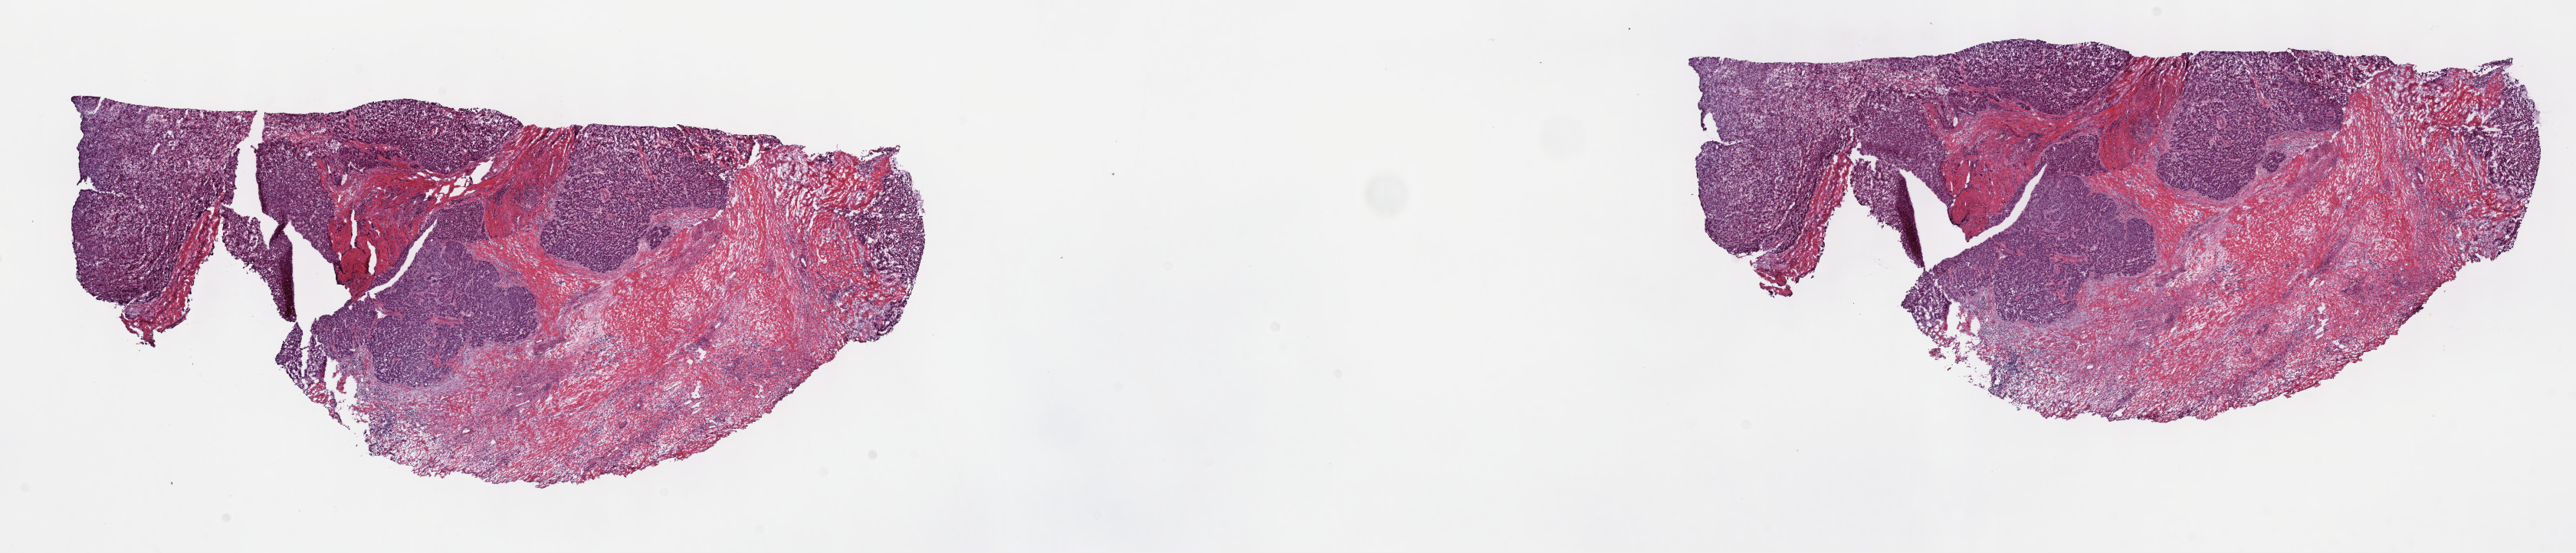
Digitized H&E-stained tissue section (whole slide) — whole scanned area (about 27.2 x 5.8 mm, from a 40x scan) shown as a low-resolution overview; frozen section from the top of the tissue portion; sample: primary tumour, liver. Female patient; age at initial diagnosis 65 years. Histologic grade: G2 (moderately differentiated). Slide review estimates, as recorded: tumour cells 50%, tumour nuclei 60%, normal cells 50%, stromal cells 0%, necrosis 0%. Infiltration values recorded for this section: lymphocyte infiltration 4%, monocyte infiltration 0%, neutrophil infiltration 0%.
TNM: T2 N0 M0. AJCC pathologic stage: II (7th edition). Diagnosis: Hepatocellular carcinoma, NOS.